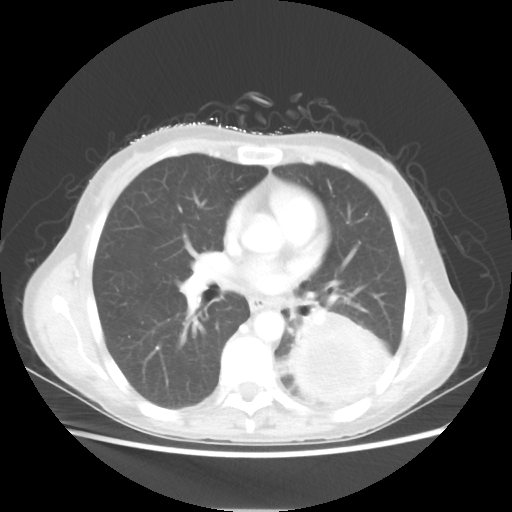
Chest CT, one axial slice. Lung window (W 1500 / L -600 HU). 5 mm slice thickness. 512 × 512 image matrix. Patient: female, 53 years. Case-level facts recorded for this patient, not image findings: clinical TNM (as recorded): T3 N0 M0.
Annotated regions visible in this slice (bounding box drawn by a radiologist):
- lung tumour (recorded histology: adenocarcinoma): bounding box [x1, y1, x2, y2] px = [288, 310, 391, 405]